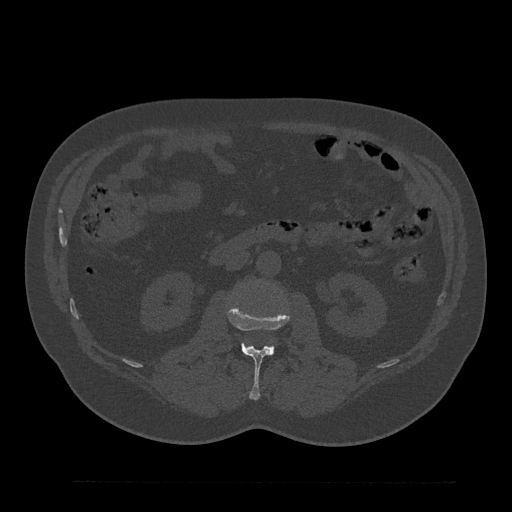
CT including the spine, one axial slice. Position 84 of 797 along the scan axis. Reconstruction kernel Br40s/3. 120 kVp. Bone window (W 1800 / L 400 HU). 512 × 512 image matrix. Patient: male, 61 years. Case-level facts recorded for this patient, not image findings: primary cancer: prostate.
Structures marked on this image (semi-automatic segmentation, software-assisted and operator-edited):
- L2 vertebra: bounding box <227,304,291,400> (left, top, right, bottom; pixels)